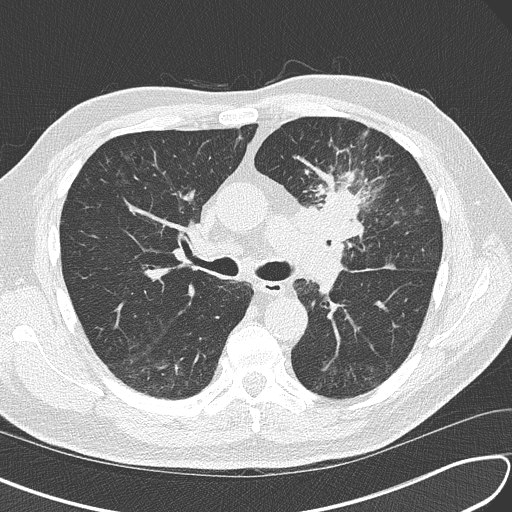
Axial slice from a low-dose chest CT screening exam, third annual screen, lung window (W 1500 / L -600 HU), 2 mm slice thickness. Male, age 67 years at enrolment.
• Lesion marked by an expert reader, box from (x=296, y=166) to (x=396, y=258) px.
• The exam's reader record, not a measurement of the box and not confirmed to be the same lesion: non-calcified nodule or mass ≥4 mm, left upper lobe, 30 × 23 mm, soft tissue attenuation, pre-existing on the prior screen: no.
• Official screen result: positive, other.